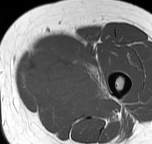
MRI of an extremity soft-tissue mass, one axial slice. Slice 20 of 57 in the series (ordered by position). MR volume resampled by the dataset authors to the PET/CT grid (not the native acquisition matrix). 152 × 144 image matrix, field of view 148 × 141 mm. Female patient. Case-level facts recorded for this patient, not image findings: histological type: pleiomorphic leiomyosarcoma; grade: intermediate; site of the primary tumour: left thigh.
Outlined on this slice (expert contour drawn on MRI and transferred to this co-registered scan by the dataset authors):
- gross tumour volume including surrounding oedema: bounding box (x1, y1, x2, y2) in pixels: (20, 46, 108, 109)
- gross tumour volume (mass): (22, 46, 101, 107)